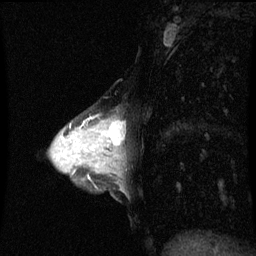
Breast MRI (dynamic contrast-enhanced), one sagittal slice. Slice 27 of 60 in the series (ordered by position). Dynamic contrast-enhanced series, image 2 of 3 at this slice position (ordered by acquisition). 1.5 T. TE 4.2 ms, TR 8.9 ms. 2 mm slice thickness. 256 × 256 image matrix. Female patient, age 33 years. From the clinical record (not read from this slice): setting: breast cancer imaged before/during neoadjuvant chemotherapy; receptor status: HER2-positive.
Structures marked on this image (semi-automatic segmentation, software-assisted and operator-edited):
- analysis volume of interest (the breast-tissue region the enhancement analysis was run in; not a lesion): box from (x=95, y=120) to (x=126, y=153) px
- tumour enhancement mask (voxels above the 70 % enhancement threshold inside the analysis volume of interest): (x=108, y=122)–(x=124, y=145)